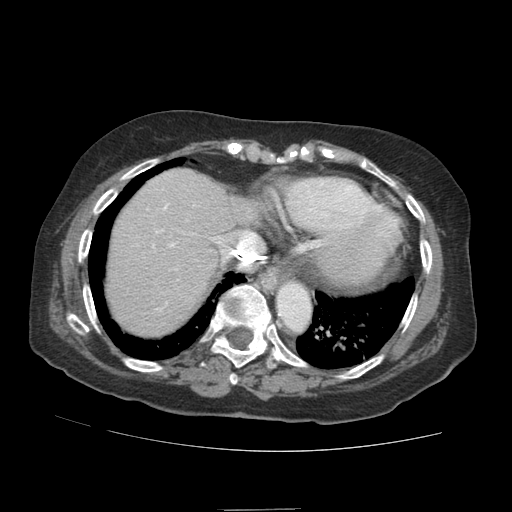
Contrast-enhanced abdominal CT (liver protocol), one axial slice. Position 76 of 89 along the scan axis. Reconstruction kernel STANDARD. 140 kVp. Soft-tissue window (W 400 / L 40 HU). 2.5 mm slice thickness. 512 × 512 image matrix. From the clinical record (not read from this slice): diagnosis: hepatocellular carcinoma (patient treated with transarterial chemoembolisation; whether this scan precedes or follows treatment is not stated here); TNM stage (as recorded): Stage-II; Child-Pugh class: A; tumour differentiation: moderately differentiated.
Annotated regions visible in this slice (semi-automatically segmented with operator editing):
- abdominal aorta: bounding box (x1, y1, x2, y2) in pixels: (277, 283, 310, 331)
- liver parenchyma outside the tumour (the mass and vessels are separate outlines, so this box may not span the whole liver): (106, 168, 259, 336)
- liver vessels: (152, 204, 222, 270)